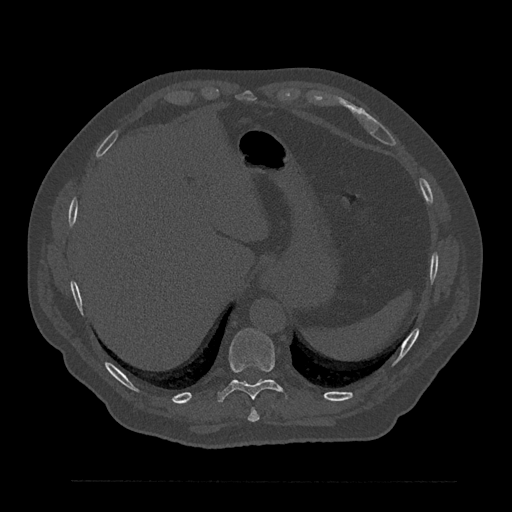
CT including the spine, one axial slice. Slice 347 of 797 in the series (ordered by position). 120 kVp. Bone window (W 1800 / L 400 HU). 0.5 mm slice thickness. 512 × 512 image matrix. Patient: male, 61 years. Case-level facts recorded for this patient, not image findings: primary cancer: prostate.
Outlined on this slice (semi-automatic segmentation, software-assisted and operator-edited):
- T10 vertebra: bounding box (x1, y1, x2, y2) in pixels: (217, 329, 288, 403)
- T9 vertebra: (247, 408, 260, 422)